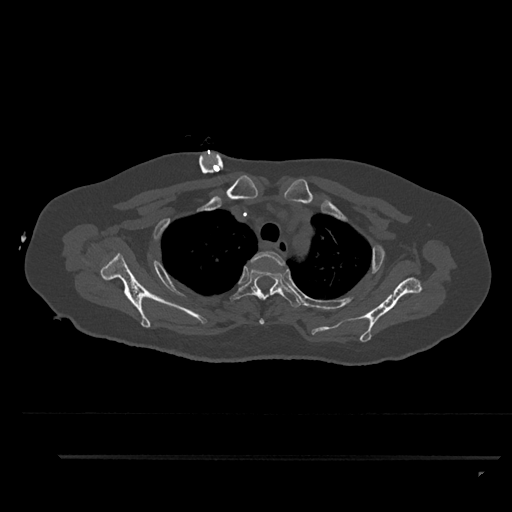
CT including the spine, one axial slice; slice 695 of 797 in the series (ordered by position); 120 kVp; bone window (W 1800 / L 400 HU); 0.5 mm slice thickness; 512 × 512 image matrix, field of view 408 × 408 mm. Female patient, age 44 years. Case-level facts recorded for this patient, not image findings: primary cancer: renal; vertebrae with lytic lesions (as recorded): L1.
Structures marked on this image (semi-automatic segmentation, software-assisted and operator-edited):
- T2 vertebra: box from (x=250, y=251) to (x=286, y=325) px
- T3 vertebra: (x=229, y=268)–(x=303, y=308)